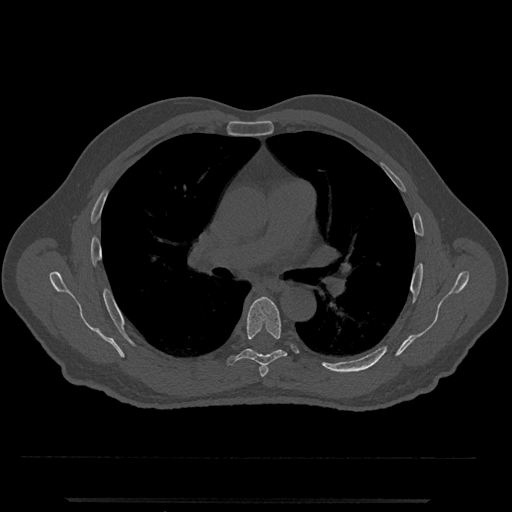
CT including the spine, one axial slice. Slice 739 of 797 in the series (ordered by position). Bone window (W 1800 / L 400 HU). 512 × 512 image matrix, field of view 419 × 419 mm. Patient: male, 63 years. Case-level facts recorded for this patient, not image findings: primary cancer: prostate.
Structures marked on this image (semi-automatically segmented with operator editing):
- T5 vertebra: box from (x=259, y=364) to (x=269, y=377) px
- T6 vertebra: (x=226, y=297)–(x=287, y=366)